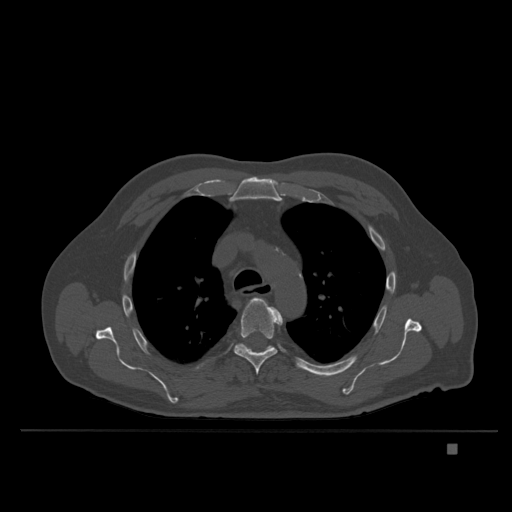
CT including the spine, one axial slice; slice 273 of 435 in the series (ordered by position); bone window (W 1800 / L 400 HU); 1.5 mm slice thickness; 512 × 512 image matrix, field of view 434 × 434 mm. Male patient, age 73 years. From the clinical record (not read from this slice): primary cancer: skin.
Outlined on this slice (semi-automatically segmented with operator editing):
- T3 vertebra: bounding box <267,346,272,350> (left, top, right, bottom; pixels)
- T5 vertebra: <233,297,283,375>
- T6 vertebra: <247,347,267,350>